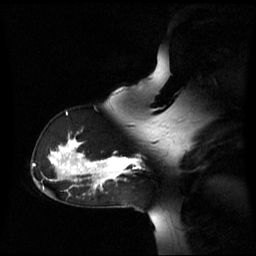
Breast MRI (dynamic contrast-enhanced), one sagittal slice; slice 43 of 60 in the series (ordered by position); dynamic contrast-enhanced series, image 2 of 3 at this slice position (ordered by acquisition); 1.5 T; TE 4.2 ms, TR 8.4 ms; 2.6 mm slice thickness; 256 × 256 image matrix, field of view 270 × 270 mm. Female patient, age 39 years. From the clinical record (not read from this slice): setting: breast cancer imaged before/during neoadjuvant chemotherapy; receptor status: triple-negative.
Outlined on this slice (semi-automatically segmented with operator editing):
- analysis volume of interest (the breast-tissue region the enhancement analysis was run in; not a lesion): bounding box (x1, y1, x2, y2) in pixels: (105, 157, 138, 179)
- tumour enhancement mask (voxels above the 70 % enhancement threshold inside the analysis volume of interest): (105, 157, 138, 179)